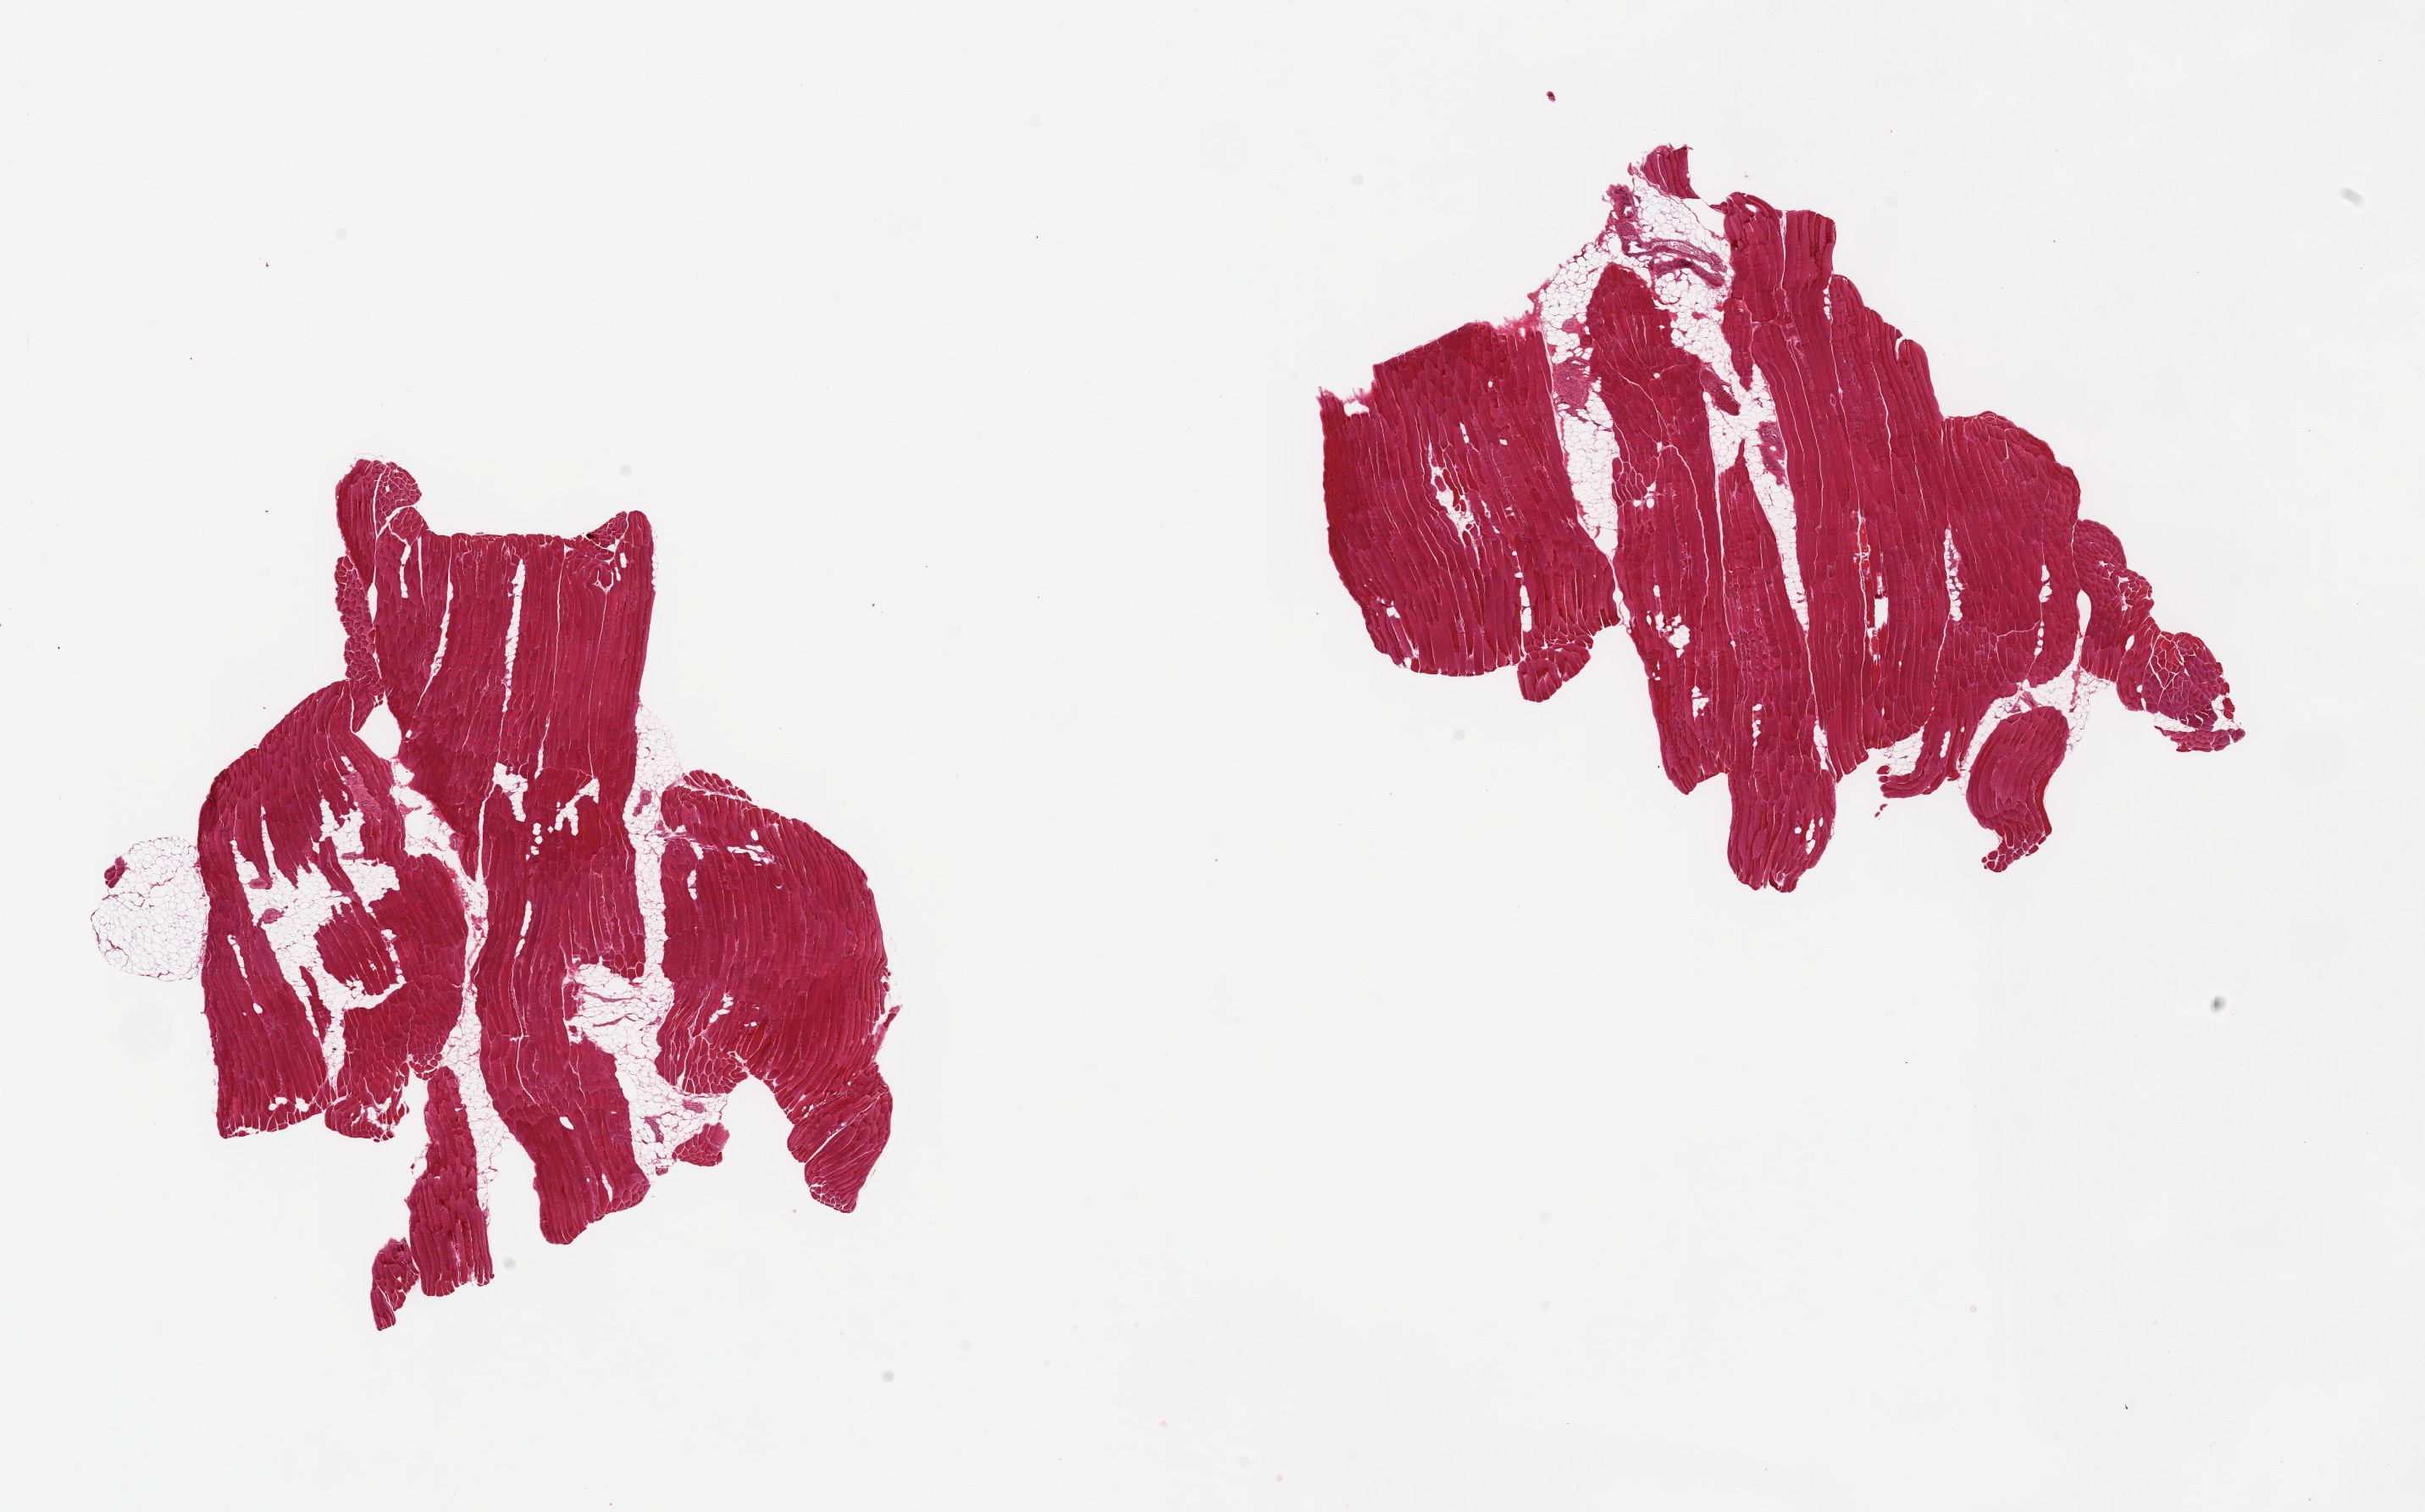
H&E whole-slide image, shown as a low-resolution overview of the whole scanned area (about 22.6 x 14.1 mm, acquisition: 20x scan), PAXgene-fixed, paraffin-embedded tissue, section of skeletal muscle (target tissue), tissue donor sample.
• review note (as recorded): 2 pieces, ~10-15% interstitial fat